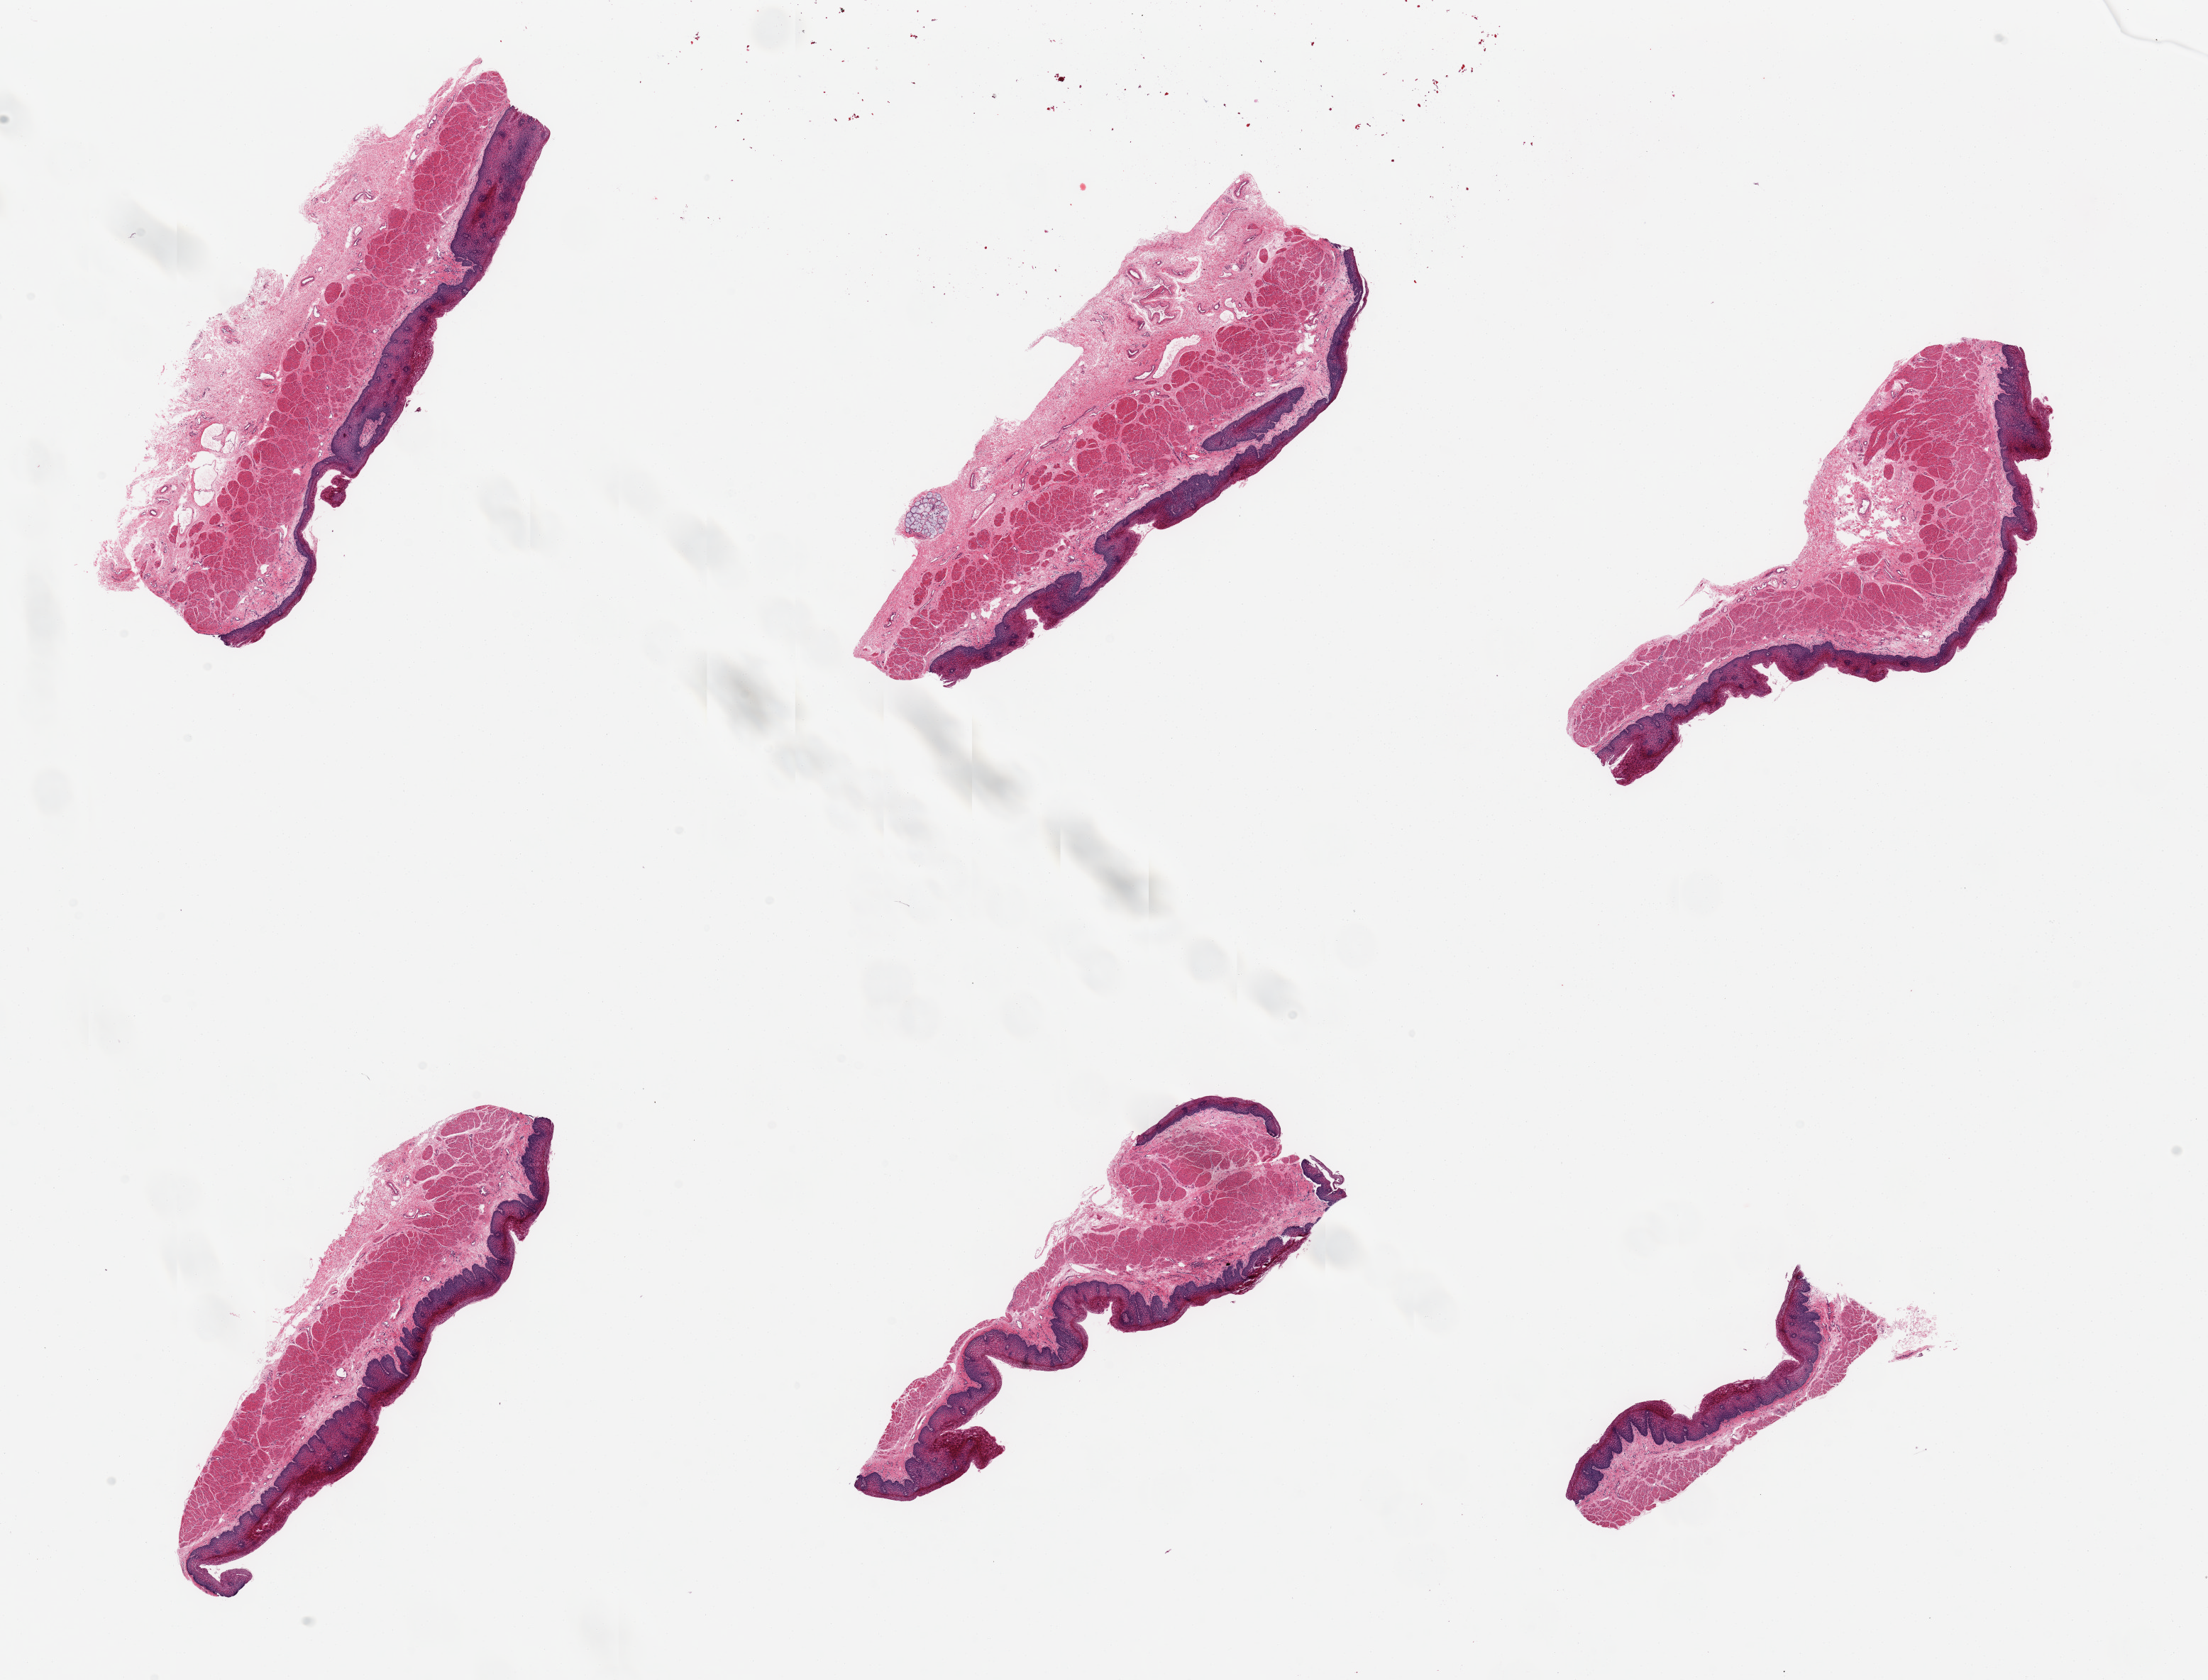
Whole-slide image, hematoxylin and eosin (H&E) stain, shown as a low-resolution overview of the whole scanned area (about 24.6 x 18.7 mm), PAXgene-fixed paraffin-embedded (PFPE) section, target tissue: esophageal mucous membrane, tissue donor sample.
• review note (as recorded): 6 pieces; intact with prominent muscularis mucosae, rare cluster of submucosal glands